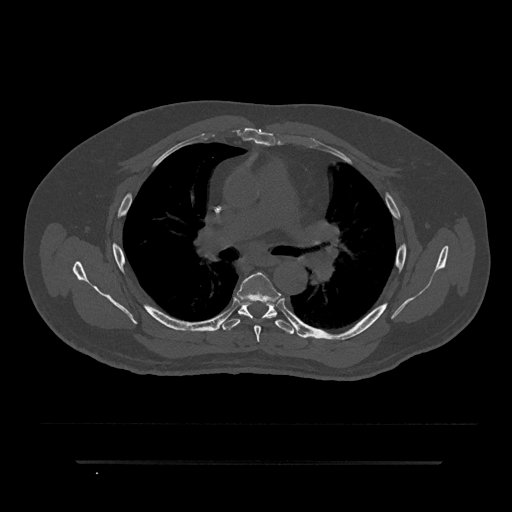
CT including the spine, one axial slice; slice 553 of 797 in the series (ordered by position); reconstruction kernel Br40s/3; 120 kVp; bone window (W 1800 / L 400 HU); 0.5 mm slice thickness; 512 × 512 image matrix, field of view 464 × 464 mm. Male patient, age 59 years. From the clinical record (not read from this slice): primary cancer: bile ducts; vertebrae with lytic lesions (as recorded): T10.
Outlined on this slice (semi-automatically segmented with operator editing):
- T5 vertebra: bounding box (x1, y1, x2, y2) in pixels: (237, 272, 278, 342)
- T6 vertebra: (221, 299, 294, 334)